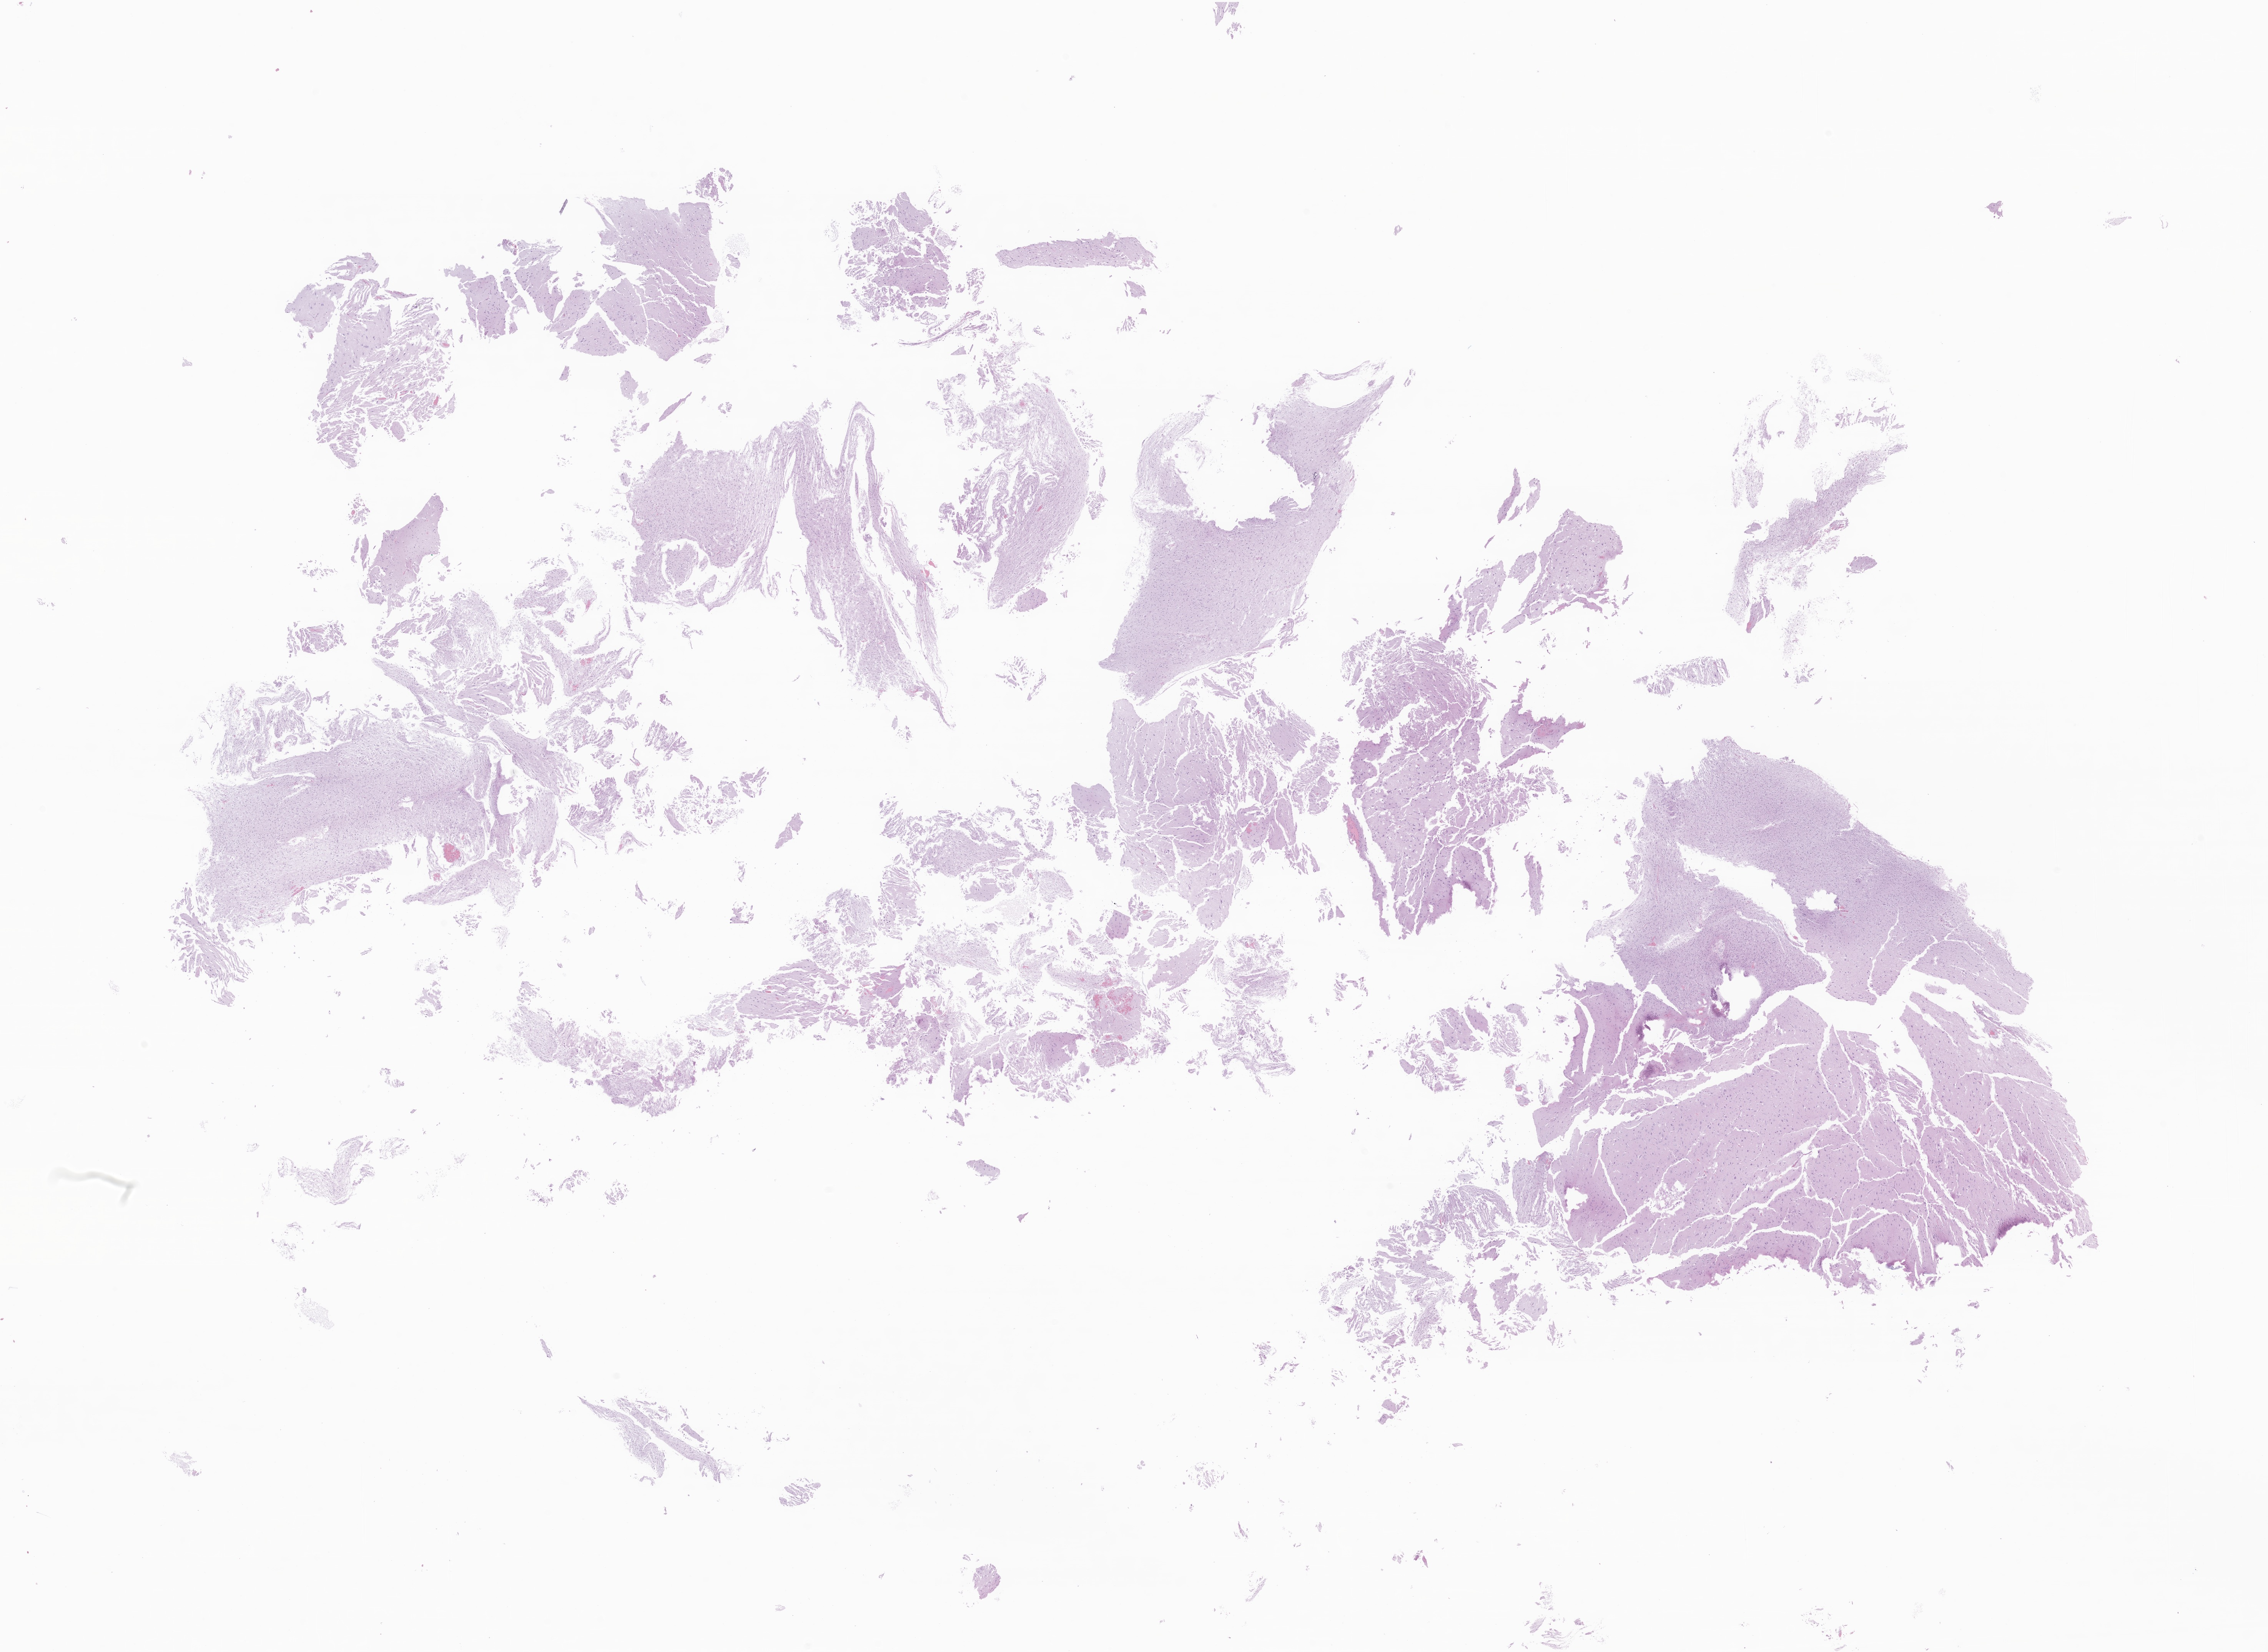
Digitized hematoxylin and eosin (H&E)-stained section of tumor tissue from the brain — low-resolution overview of the scanned area, about 24.9 x 18.1 mm. FFPE section. Female patient, age 45 months (3 years 9 months).
Diagnosis (ICD-O-3 morphology term): Glioma, malignant.